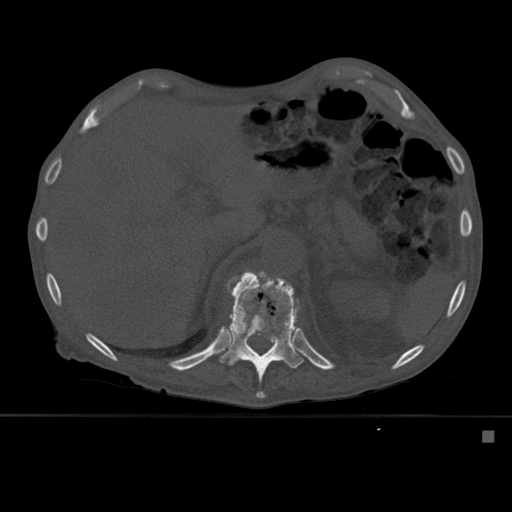
CT including the spine, one axial slice; position 277 of 527 along the scan axis; bone window (W 1800 / L 400 HU); 512 × 512 image matrix. Patient: male, 78 years. From the clinical record (not read from this slice): primary cancer: prostate.
Outlined on this slice (semi-automatic segmentation, software-assisted and operator-edited):
- T11 vertebra: bounding box [x1, y1, x2, y2] px = [223, 271, 251, 327]
- T12 vertebra: [219, 269, 304, 398]